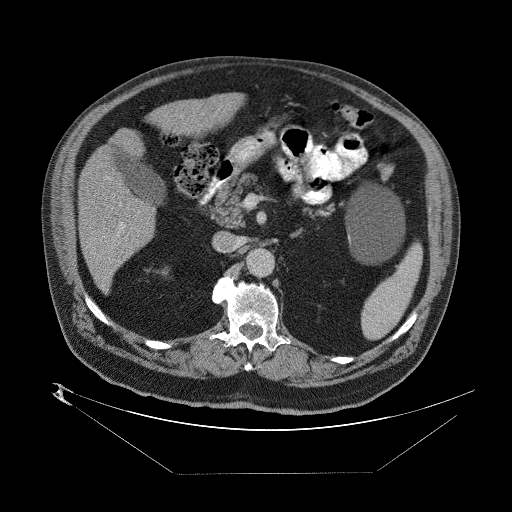
Contrast-enhanced abdominal CT (liver protocol), one axial slice; slice 32 of 89 in the series (ordered by position); one of 2 acquisitions stored at this slice position; soft-tissue window (W 400 / L 40 HU); 512 × 512 image matrix. From the clinical record (not read from this slice): diagnosis: hepatocellular carcinoma (patient treated with transarterial chemoembolisation; whether this scan precedes or follows treatment is not stated here); TNM stage (as recorded): Stage-II; Child-Pugh class: B; tumour nodularity: multinodular; tumour size: 4 cm.
Annotated regions visible in this slice (semi-automatic segmentation, software-assisted and operator-edited):
- abdominal aorta: bounding box <248,251,272,276> (left, top, right, bottom; pixels)
- liver parenchyma outside the tumour (the mass and vessels are separate outlines, so this box may not span the whole liver): <76,97,236,294>
- liver vessels: <91,182,139,259>